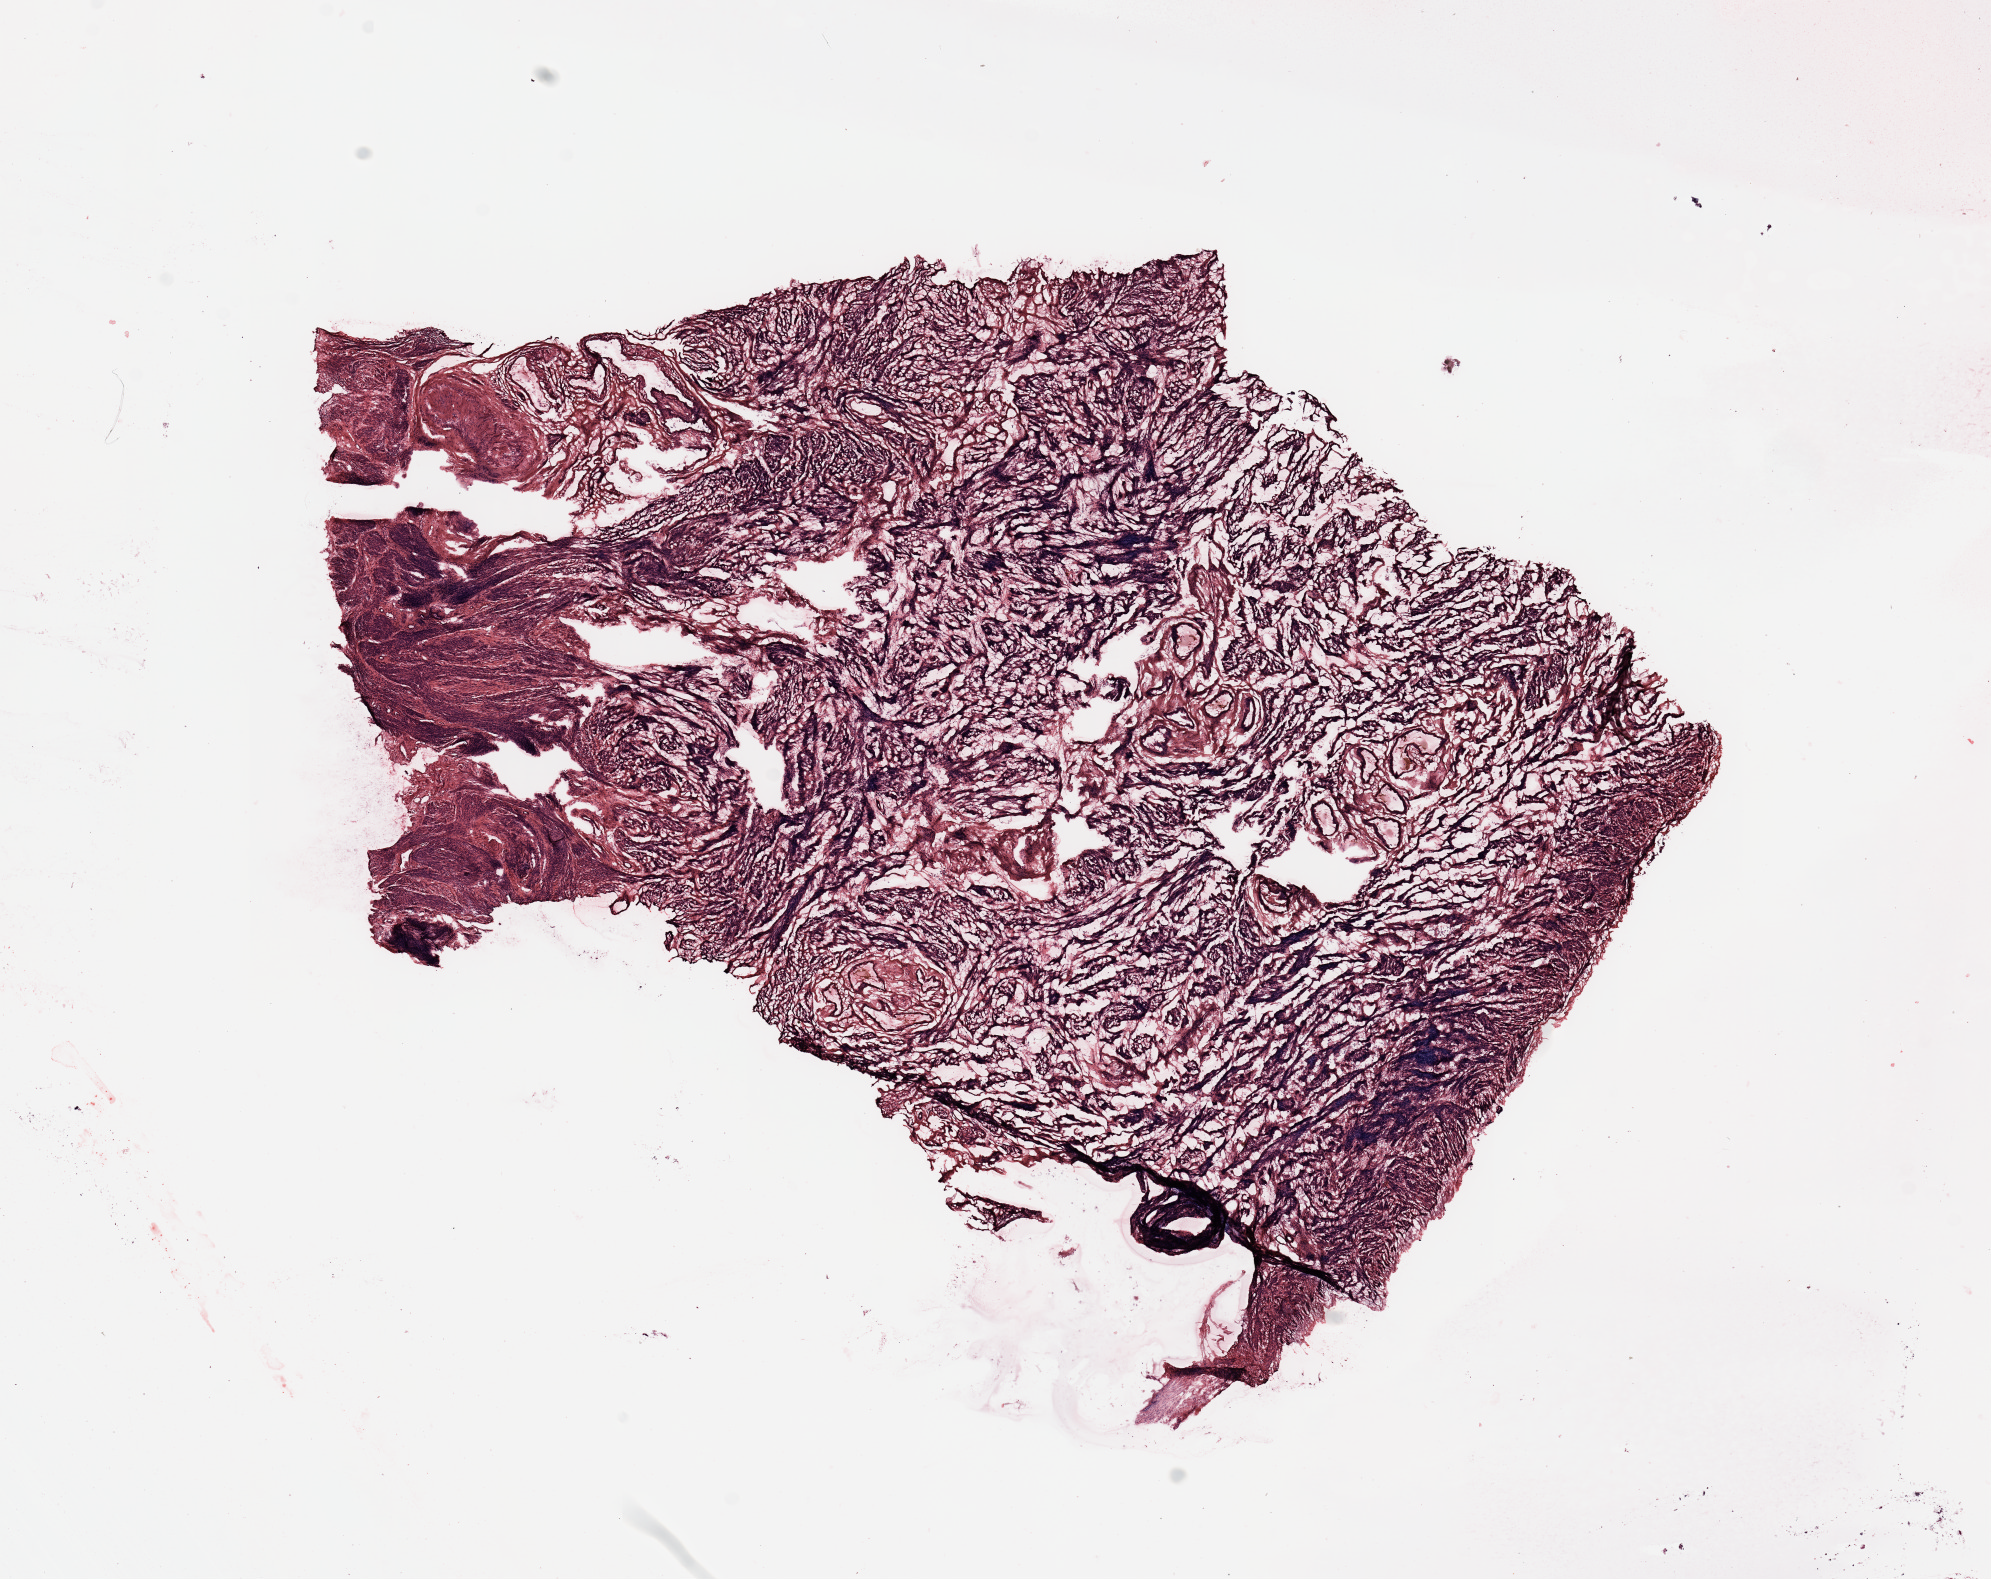
Digitized H&E-stained tissue section (whole slide), low-resolution overview of the scanned area, about 15.8 x 12.5 mm (slide scanned at 20x); normal (non-tumour) tissue sample, uterus. 70-year-old female patient.
- this section: normal (non-tumour) tissue from the same patient
- patient diagnosis: Endometrioid adenocarcinoma, NOS